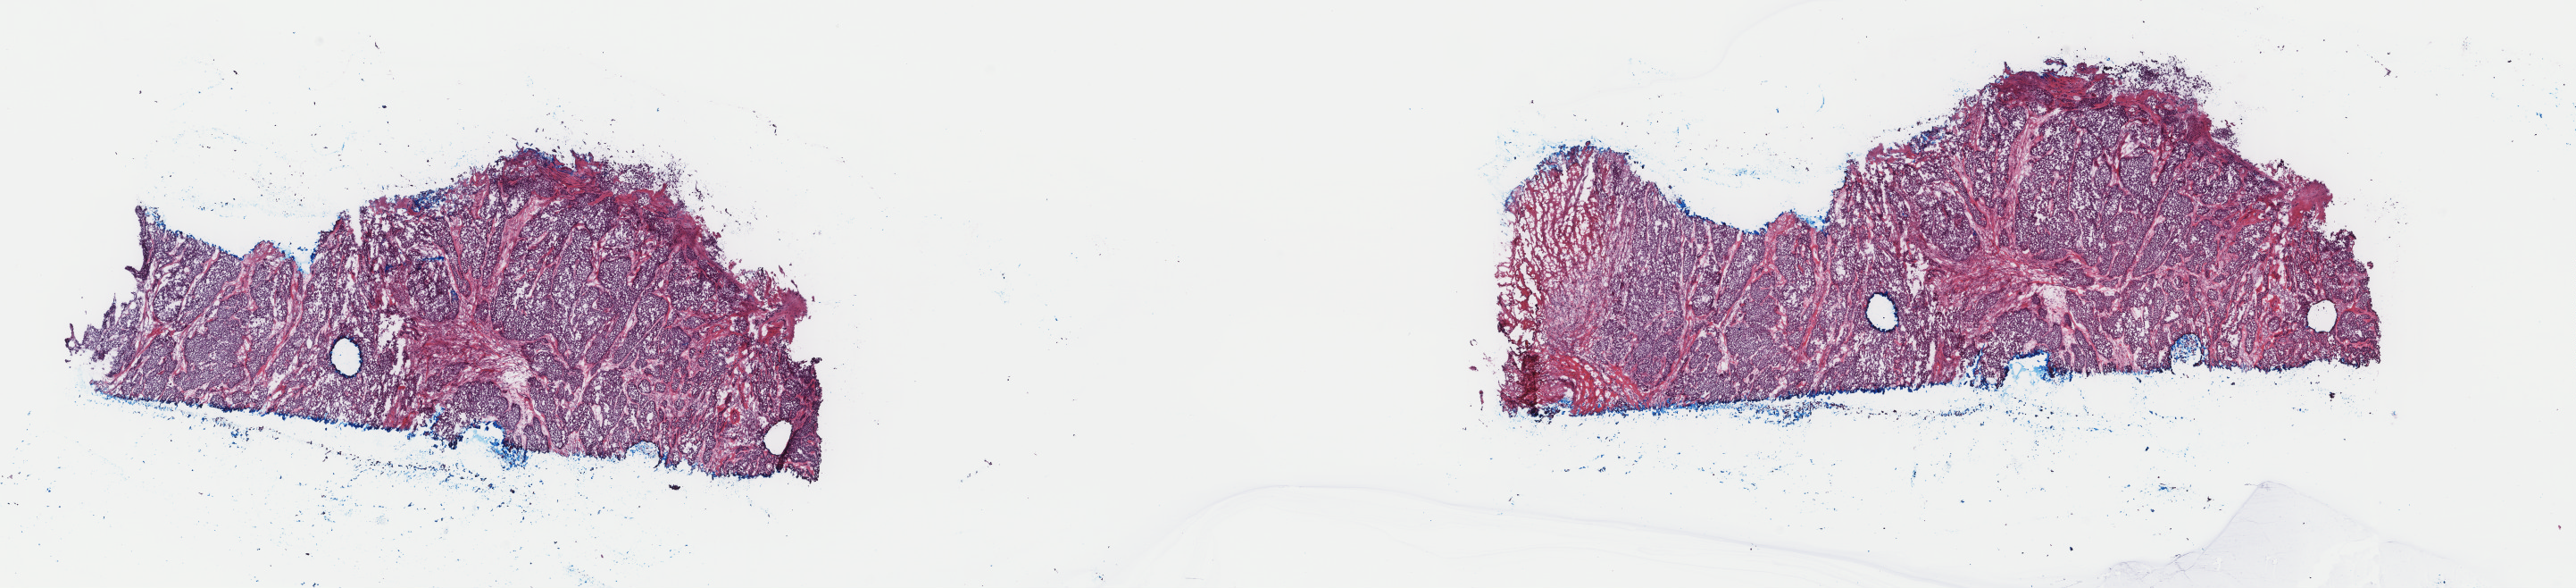
H&E-stained whole-slide image — whole scanned area (about 22.9 x 5.2 mm, from a 40x scan) shown as a low-resolution overview. Frozen section from the top of the tissue portion. Primary tumour sample from the bladder. Female, age 83 years at initial diagnosis. Histologic grade: high grade. Composition of this section per pathologist review: tumour cells 100%, tumour nuclei 90%, normal cells 0%, stromal cells 0%, necrosis 0%. Inflammatory infiltration, as recorded: lymphocyte infiltration 2%, monocyte infiltration 0%, neutrophil infiltration 0%.
AJCC pathologic stage: III (7th edition). Pathologic diagnosis: Transitional cell carcinoma.